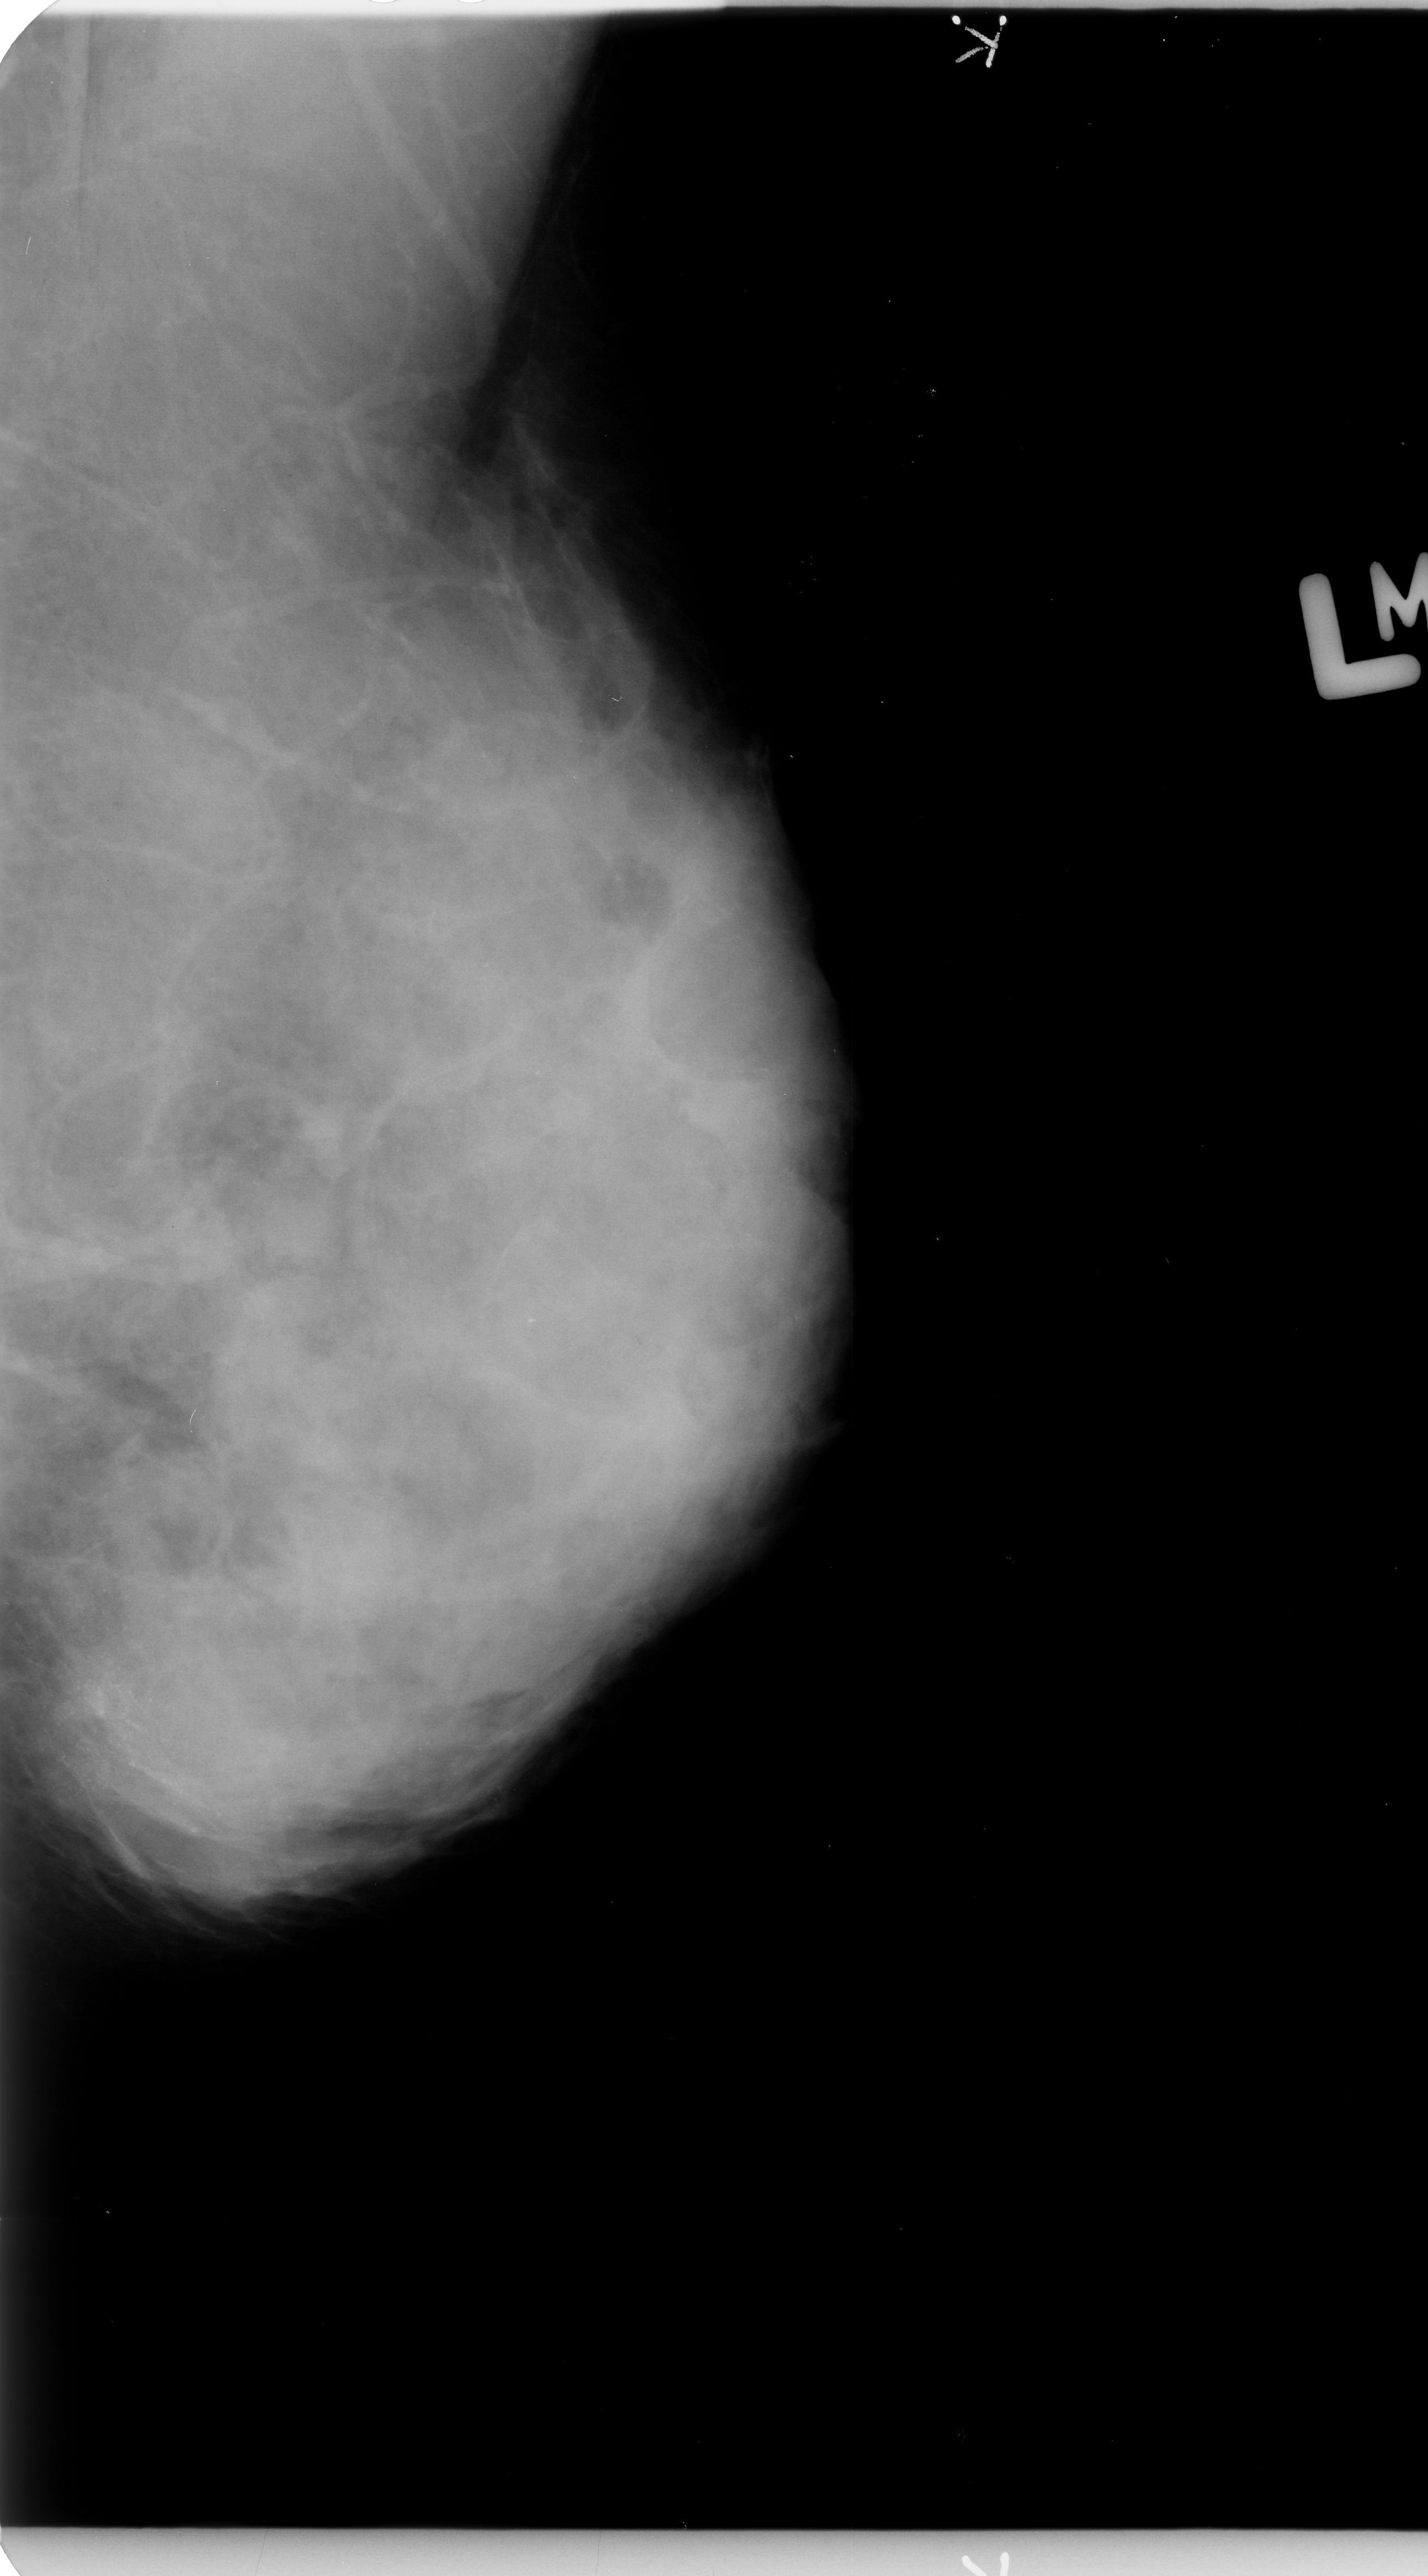
Mammogram (digitized film). Left breast. Mediolateral oblique (MLO) view. Breast composition: extremely dense (BI-RADS density category 4 of 4). 1428 × 2576 image matrix.
Expert-marked regions of interest on this image (one box per marked abnormality):
- calcifications, morphology pleomorphic, distribution clustered; BI-RADS assessment category 4; pathology result (as recorded, not read from the image): malignant: bounding box <0,1498,273,1911> (left, top, right, bottom; pixels)